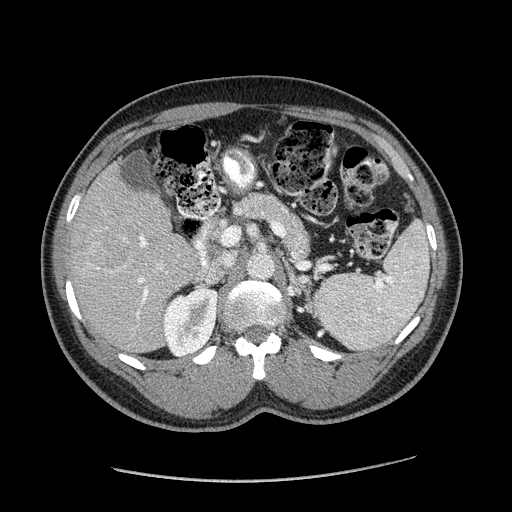
Contrast-enhanced abdominal CT (liver protocol), one axial slice; 120 kVp; soft-tissue window (W 400 / L 40 HU); 2.5 mm slice thickness; 512 × 512 image matrix. From the clinical record (not read from this slice): diagnosis: hepatocellular carcinoma (patient treated with transarterial chemoembolisation; whether this scan precedes or follows treatment is not stated here); TNM stage (as recorded): Stage-I; Child-Pugh class: A; tumour differentiation: well differentiated; tumour size: 3.1 cm.
Outlined on this slice (semi-automatically segmented with operator editing):
- liver parenchyma outside the tumour (the mass and vessels are separate outlines, so this box may not span the whole liver): bounding box <68,161,204,352> (left, top, right, bottom; pixels)
- mass: <85,228,134,273>
- liver vessels: <97,230,179,319>